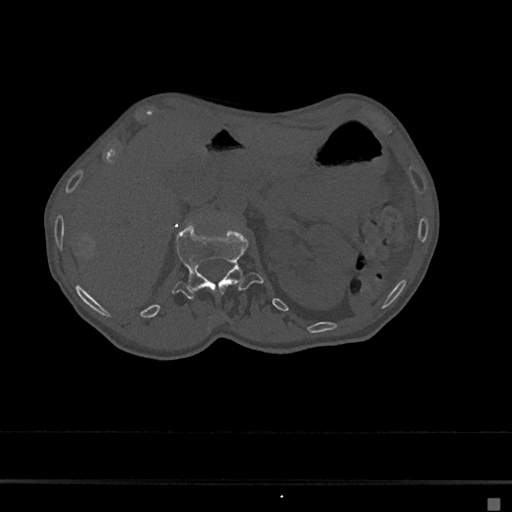
CT including the spine, one axial slice; position 72 of 797 along the scan axis; 120 kVp; bone window (W 1800 / L 400 HU); 0.5 mm slice thickness; 512 × 512 image matrix, field of view 360 × 360 mm. Female patient, age 68 years. Case-level facts recorded for this patient, not image findings: primary cancer: renal.
Outlined on this slice (semi-automatic segmentation, software-assisted and operator-edited):
- L1 vertebra: box from (x=172, y=221) to (x=264, y=299) px